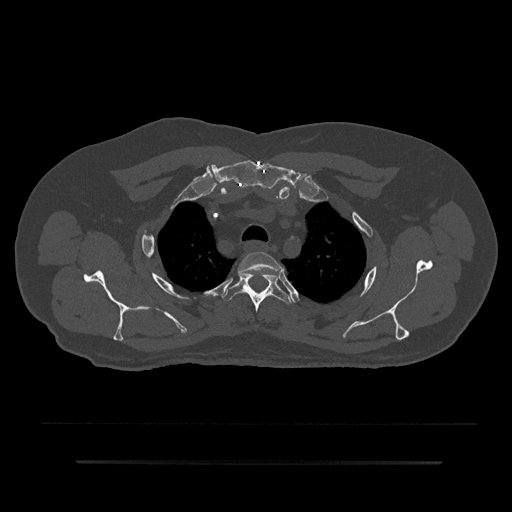
CT including the spine, one axial slice. Position 670 of 797 along the scan axis. 120 kVp. Bone window (W 1800 / L 400 HU). 512 × 512 image matrix. Patient: male, 59 years. From the clinical record (not read from this slice): primary cancer: bile ducts.
Outlined on this slice (semi-automatically segmented with operator editing):
- T2 vertebra: bounding box <238,252,281,292> (left, top, right, bottom; pixels)
- T3 vertebra: <222,272,292,313>